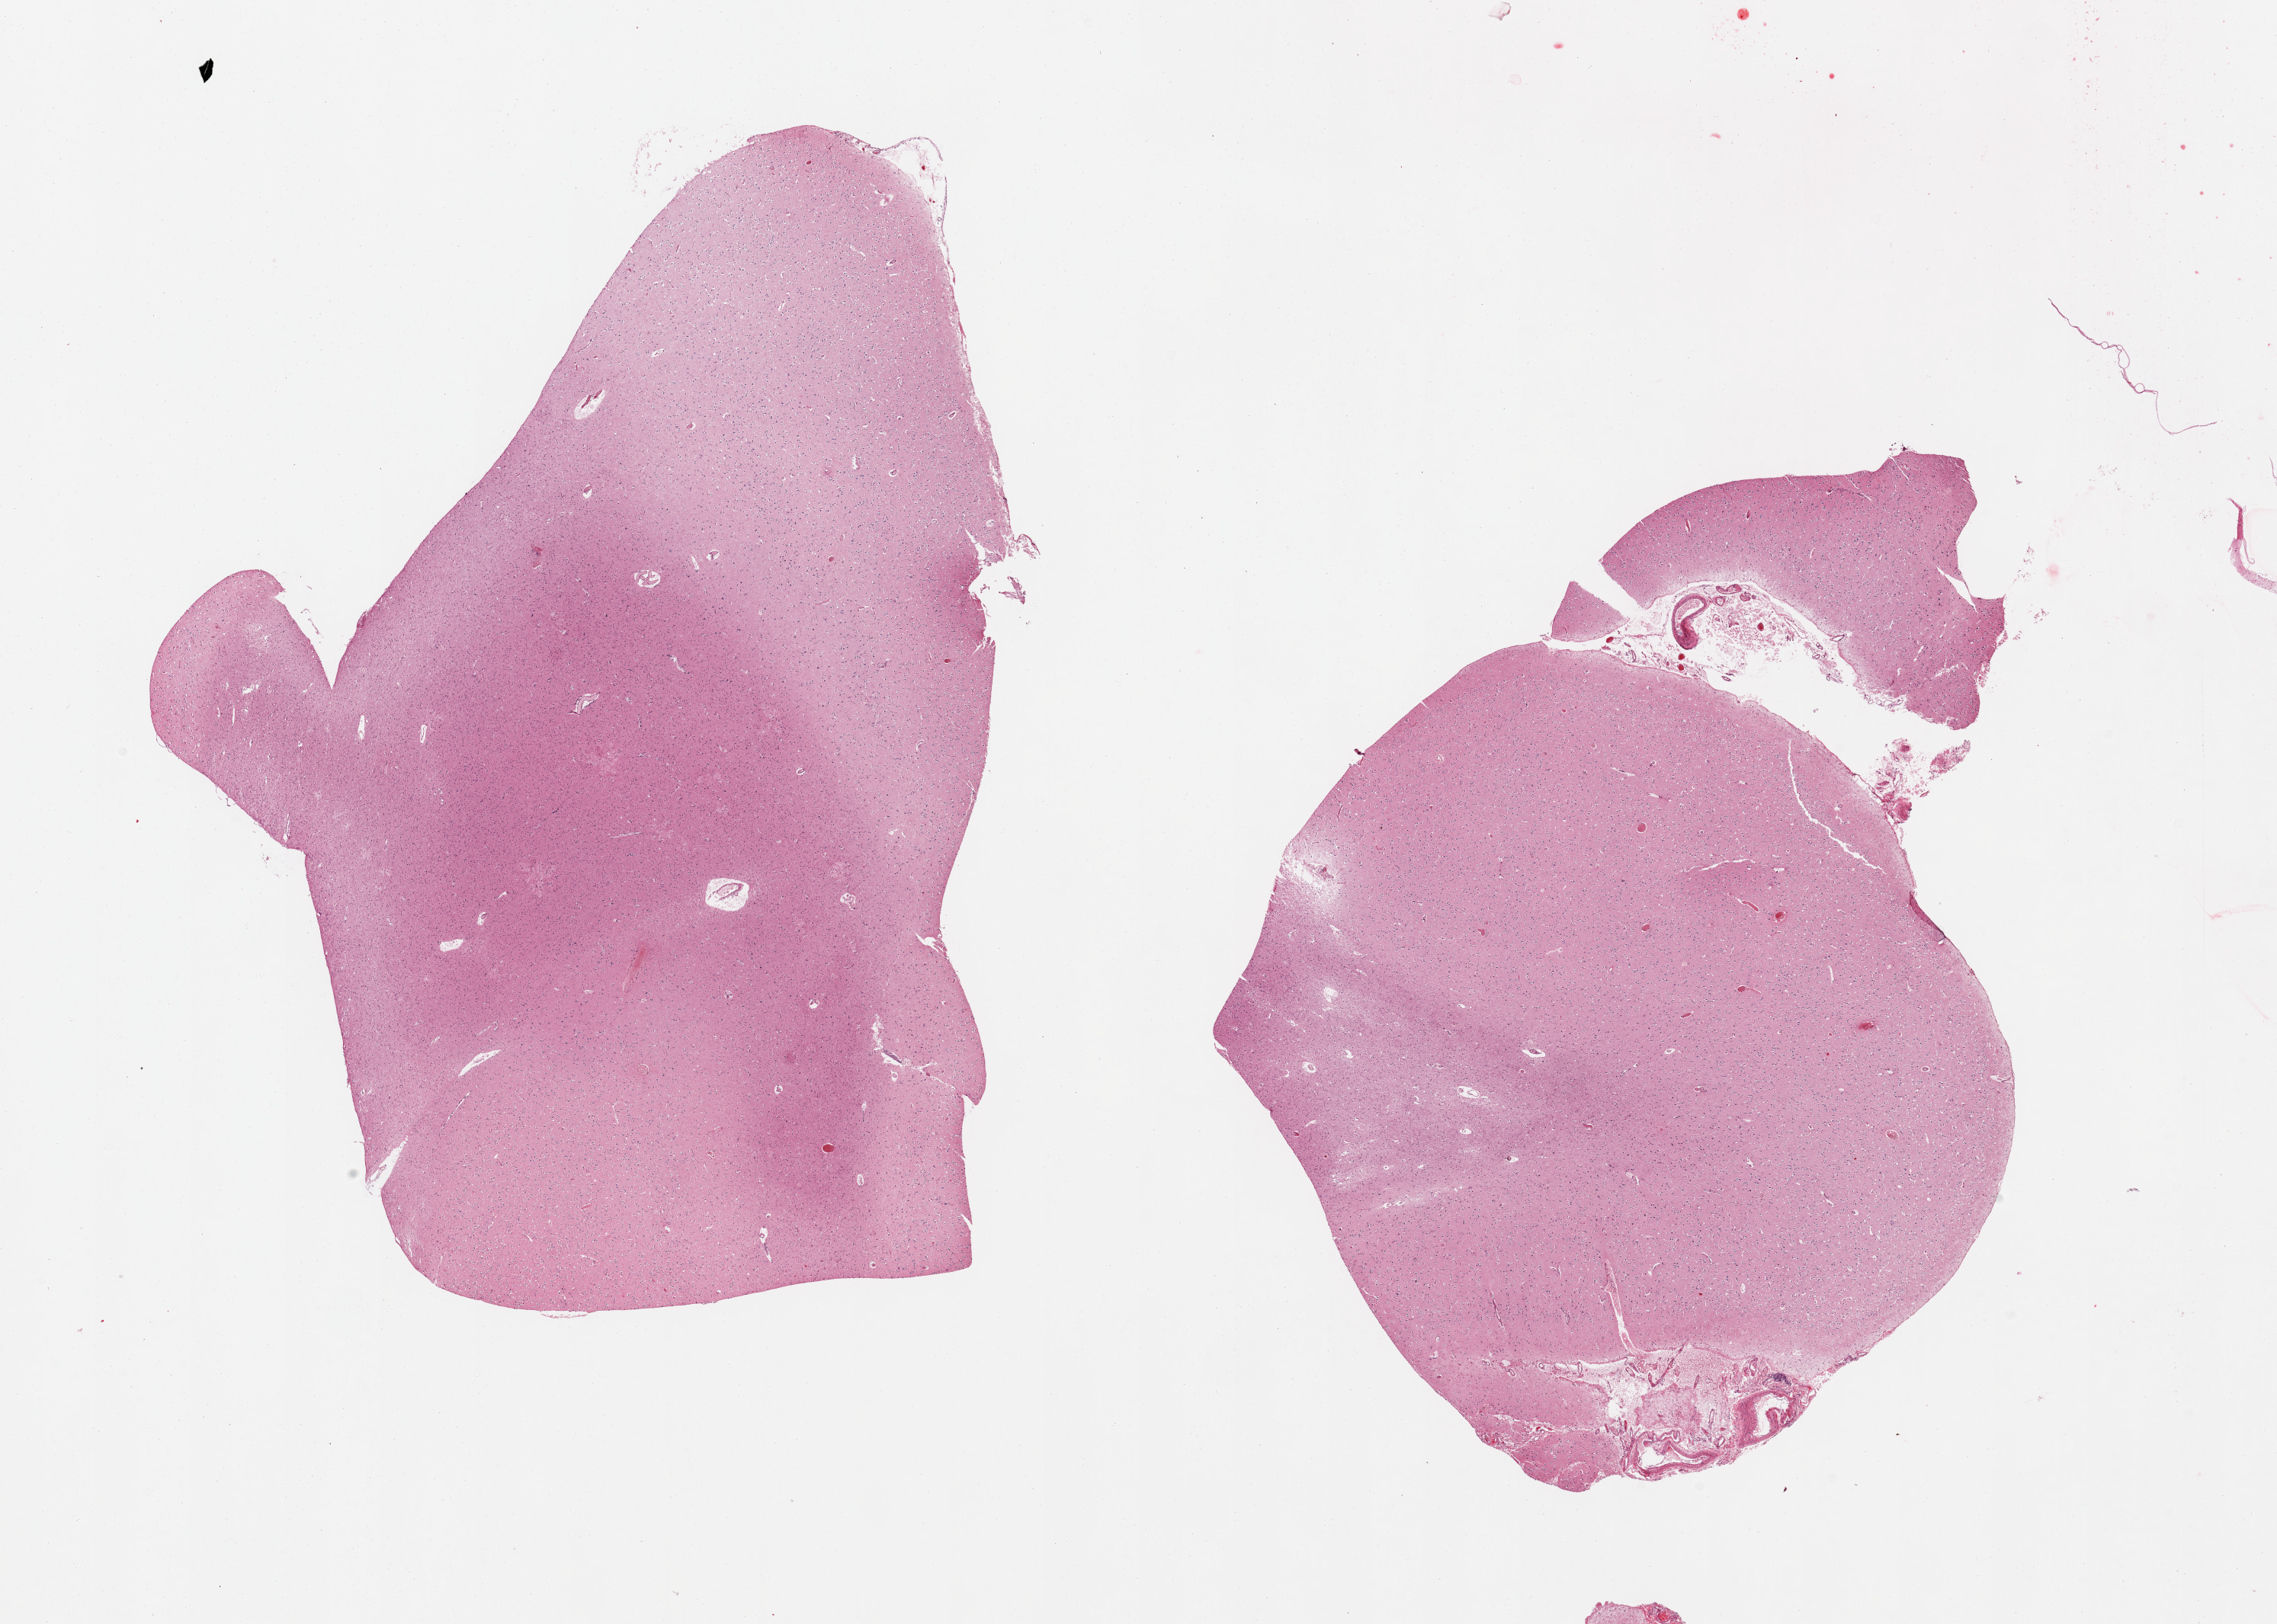
Digitized haematoxylin and eosin-stained section — a low-resolution overview of the entire scanned area, about 23.6 x 16.9 mm, PAXgene-fixed, paraffin-embedded tissue, section of cerebral cortex (target tissue), donor tissue sample. Donor sex: male.
Review note (as recorded): 2 pieces.